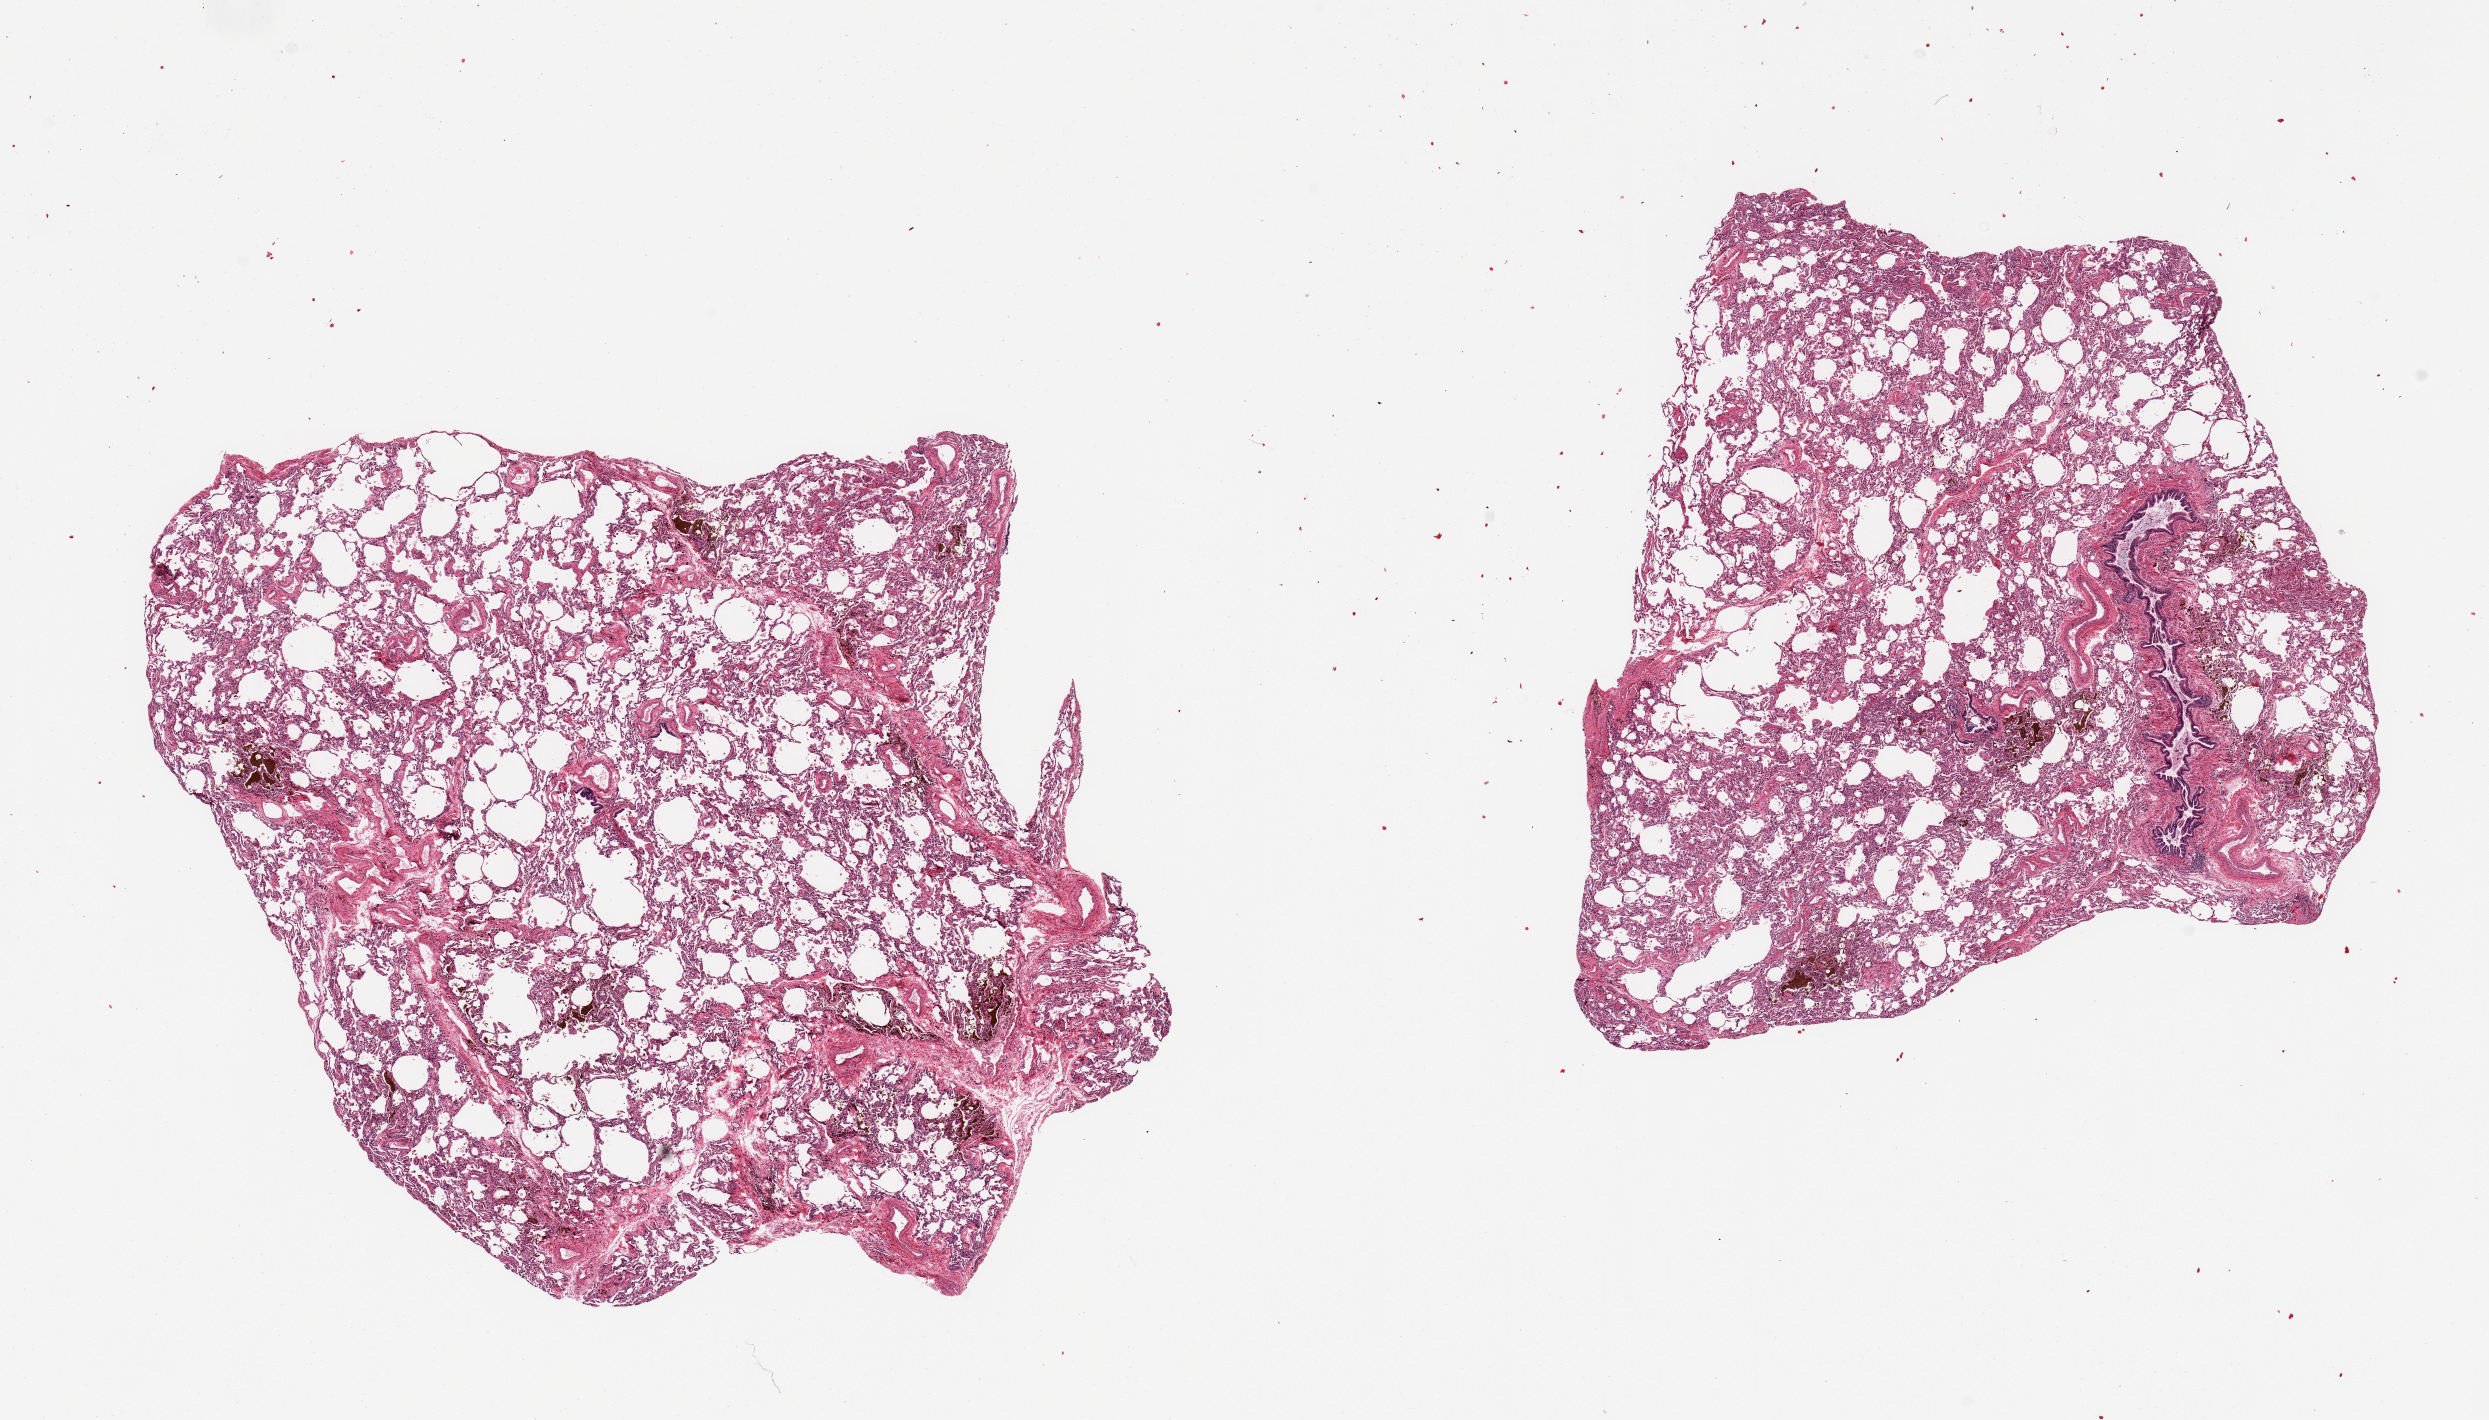
H&E whole-slide image — whole scanned area (about 19.7 x 11.2 mm) shown as a low-resolution overview. PAXgene-fixed paraffin-embedded (PFPE) section. Target tissue: lung. Donor tissue sample. Donor: male.
- review note (as recorded): 2 pieces; mild emphysema; small foci of pigmented alveolar macrophages